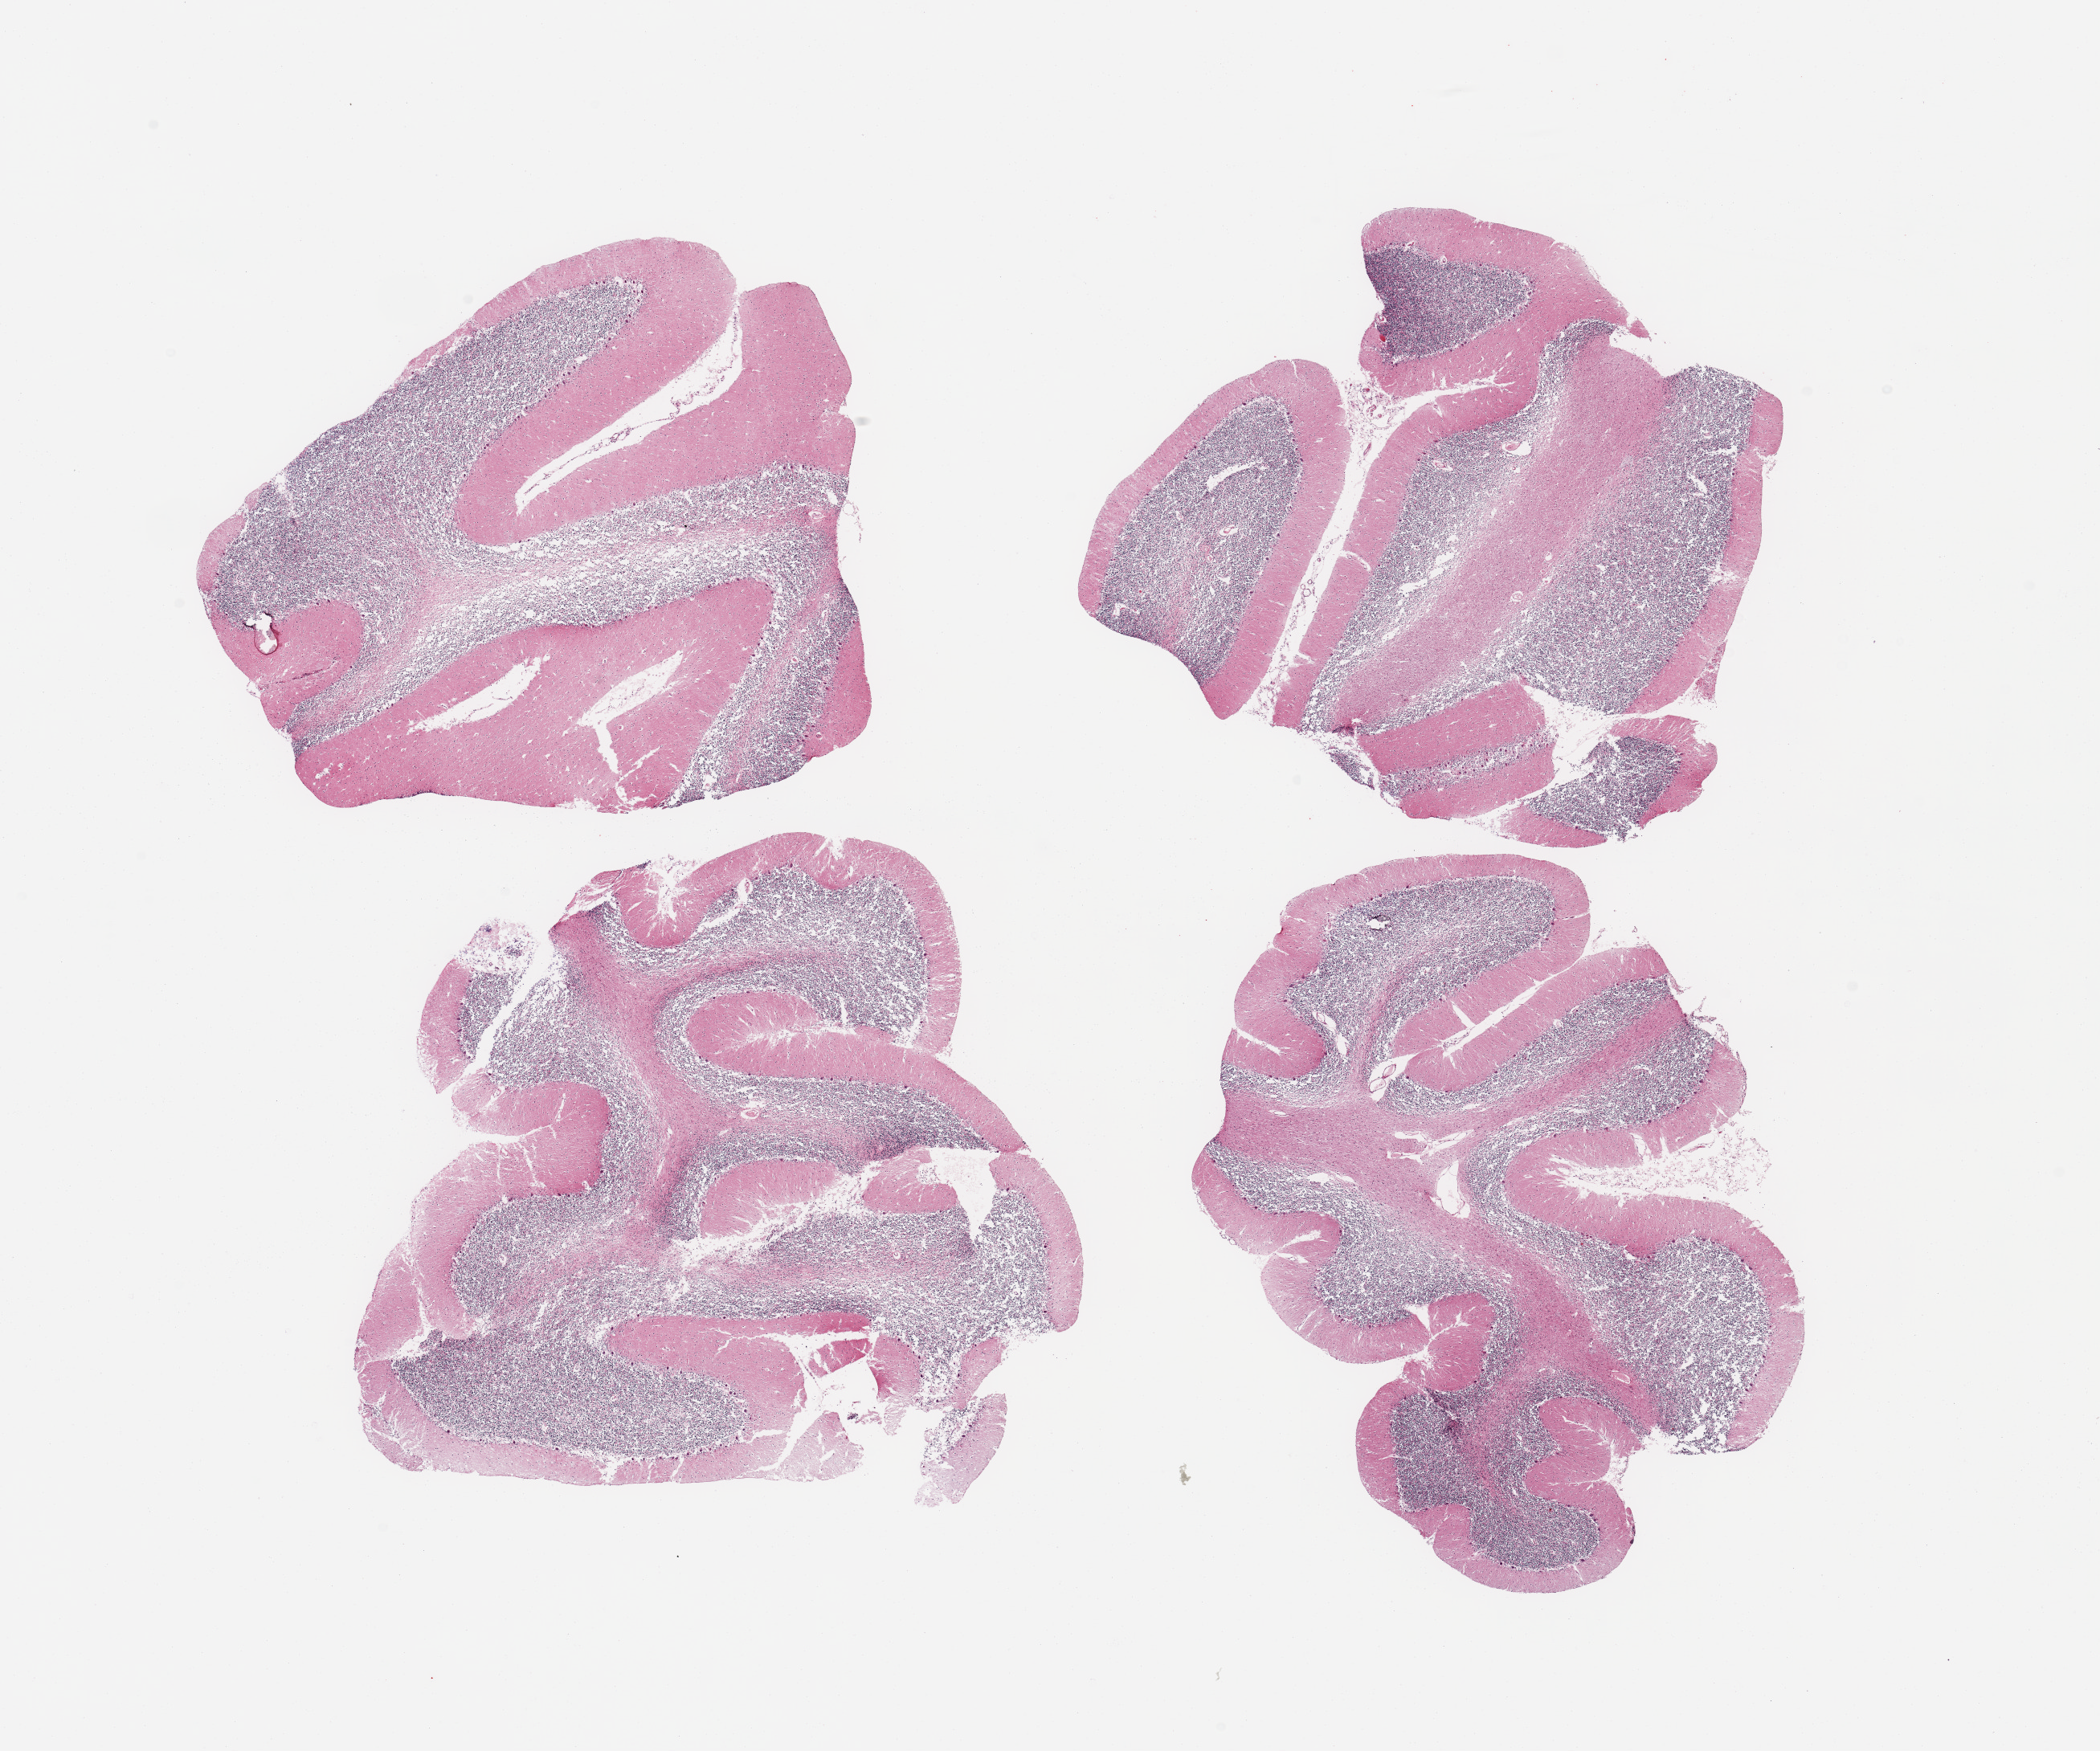
Haematoxylin and eosin whole-slide image, brightfield, a low-resolution overview of the entire scanned area, about 20.7 x 17.2 mm; PAXgene-fixed paraffin-embedded (PFPE) section; section of cerebellum (target tissue); donor tissue sample.
- reviewer comment on this tissue sample: 4 pieces